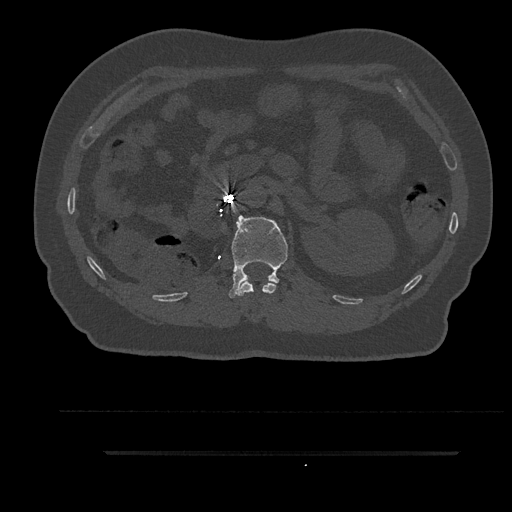
CT including the spine, one axial slice; reconstruction kernel Br40s/3; 120 kVp; bone window (W 1800 / L 400 HU); 0.5 mm slice thickness; 512 × 512 image matrix, field of view 432 × 432 mm. Patient: male, 63 years. Case-level facts recorded for this patient, not image findings: primary cancer: renal; vertebrae with lytic lesions (as recorded): T8.
Outlined on this slice (semi-automatically segmented with operator editing):
- L1 vertebra: bounding box (x1, y1, x2, y2) in pixels: (228, 215, 288, 299)
- T12 vertebra: (238, 280, 276, 296)